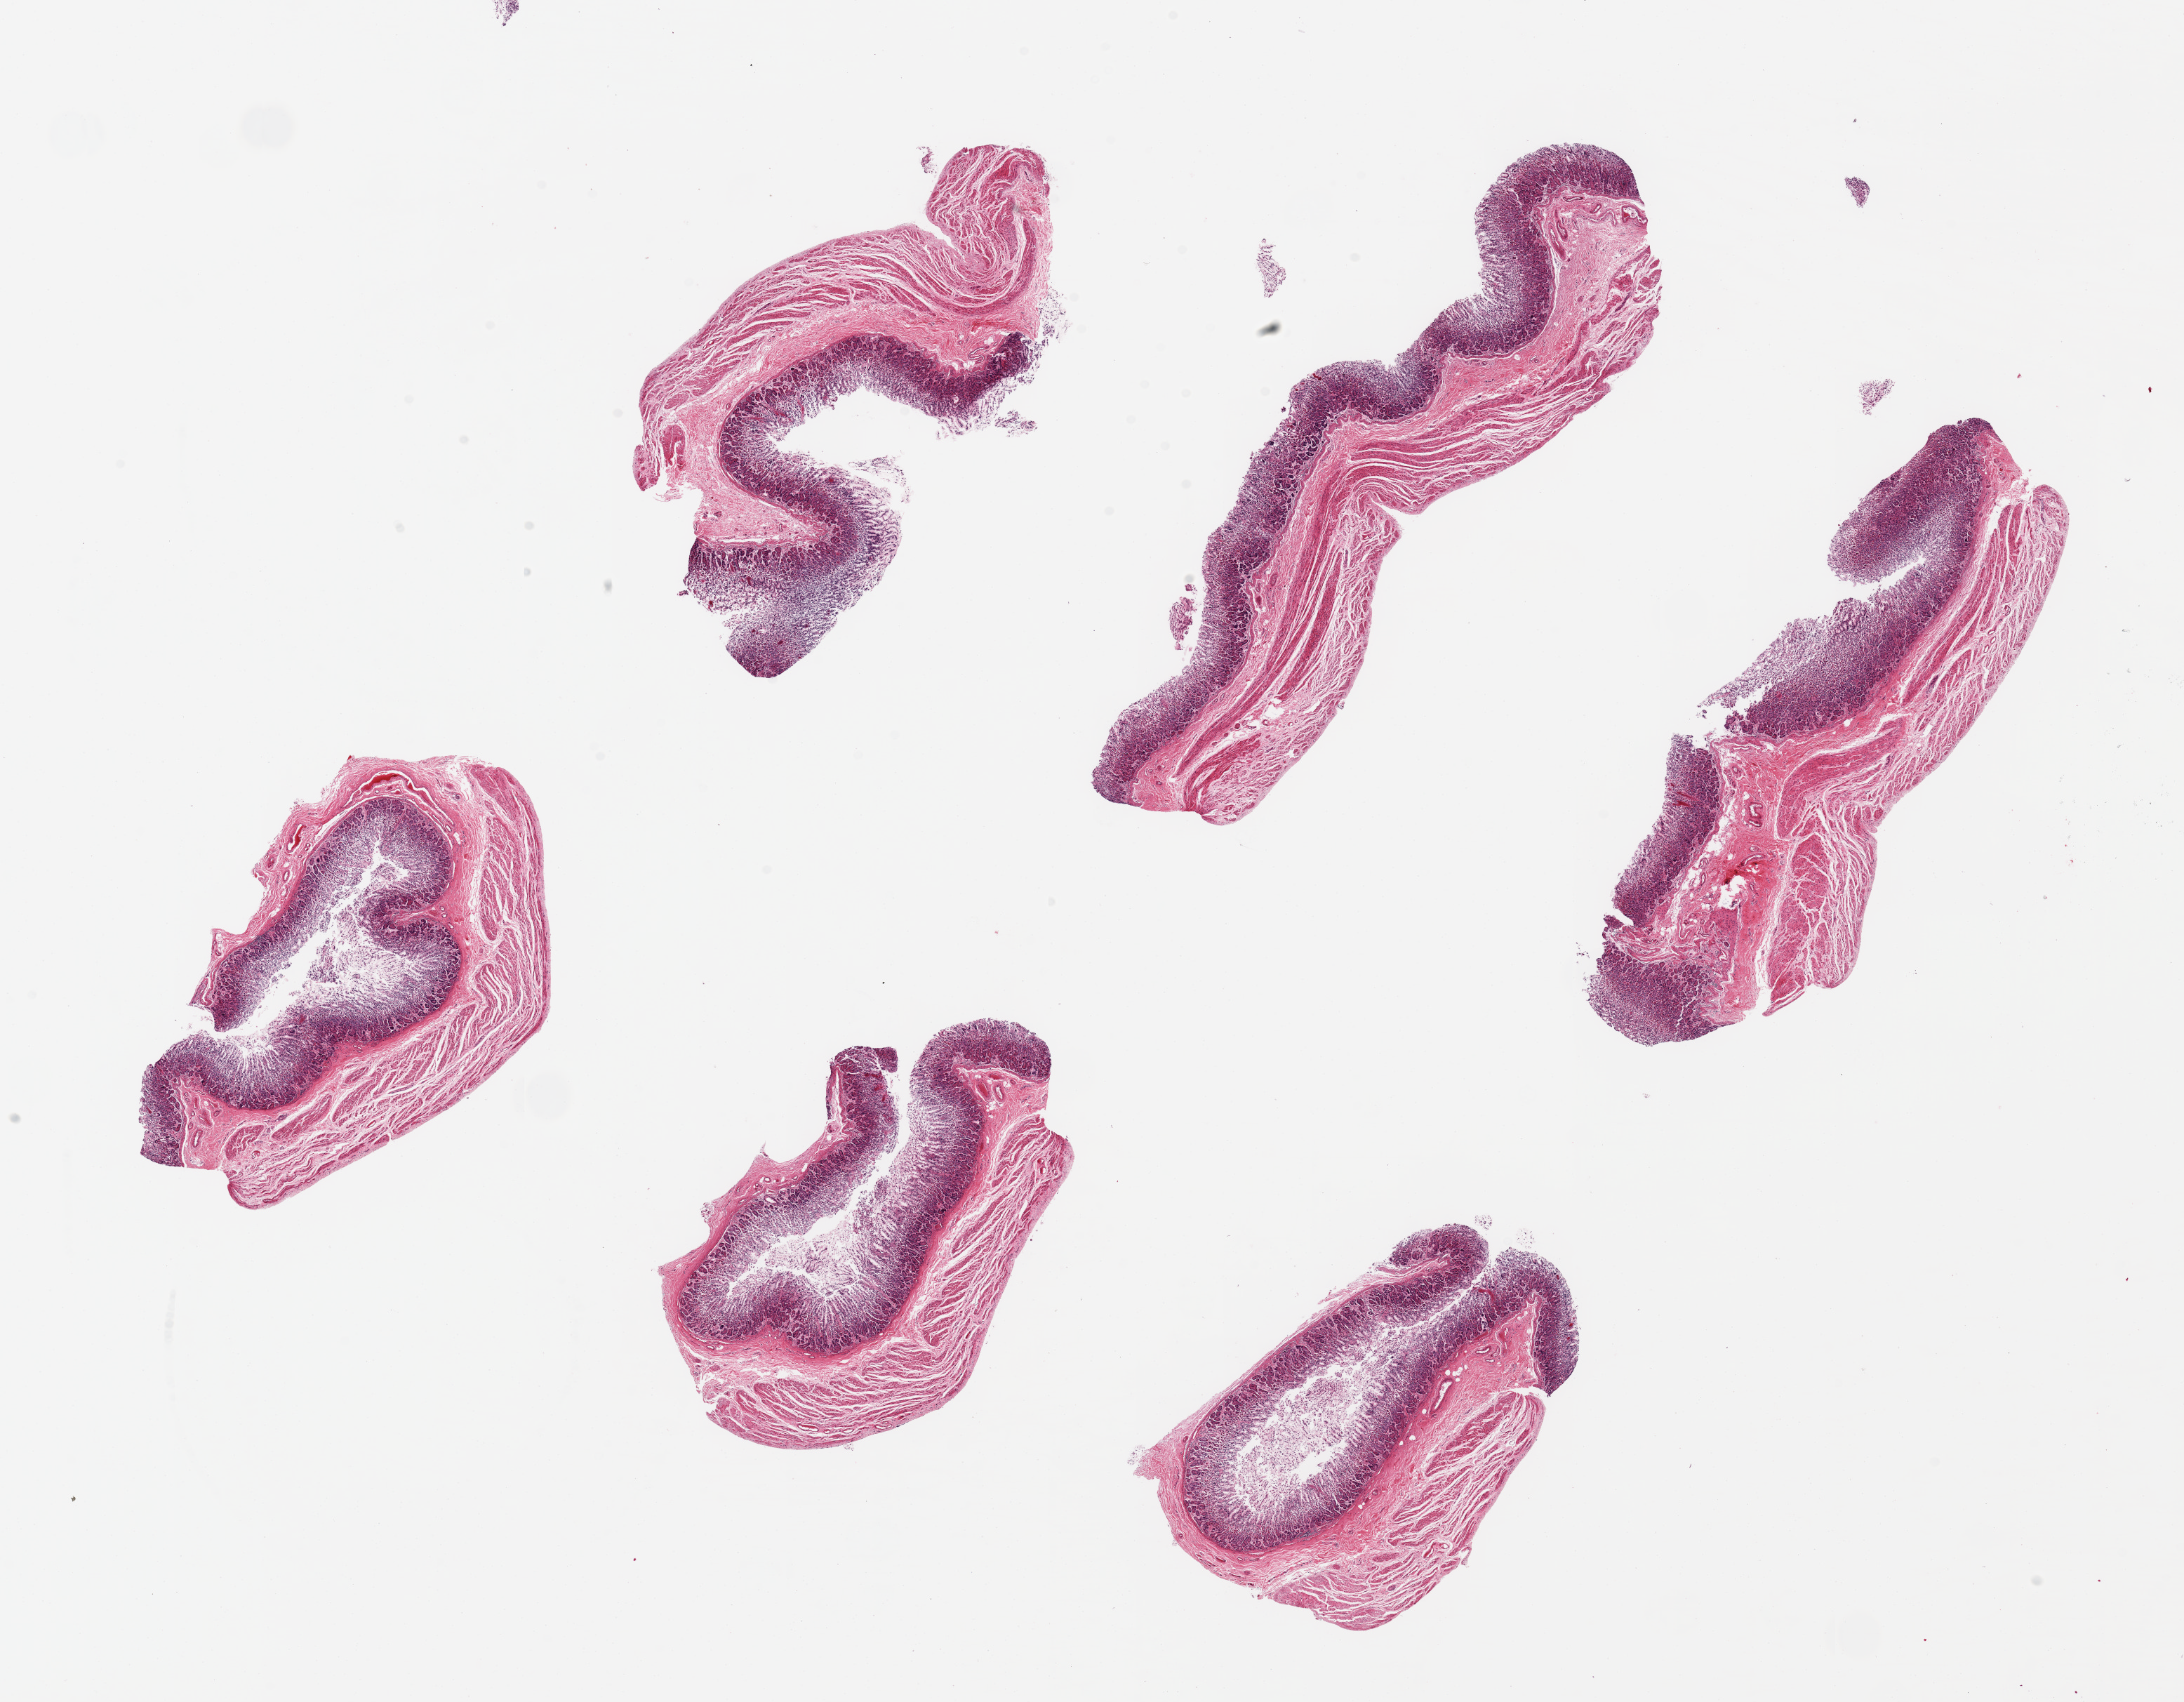
Whole-slide image, hematoxylin and eosin (H&E) stain, whole scanned area (about 24.6 x 19.2 mm, from a 20x scan) shown as a low-resolution overview; PAXgene-fixed paraffin-embedded (PFPE) section; section of stomach (target tissue); donor tissue sample. Donor sex: male.
• pathologist's review note for this sample: 6 ~9x1.5mm pieces. Mucosa poorly preserved over-all, superficial portions sloughed and badly autolyzed-- ~20-30% of thickness